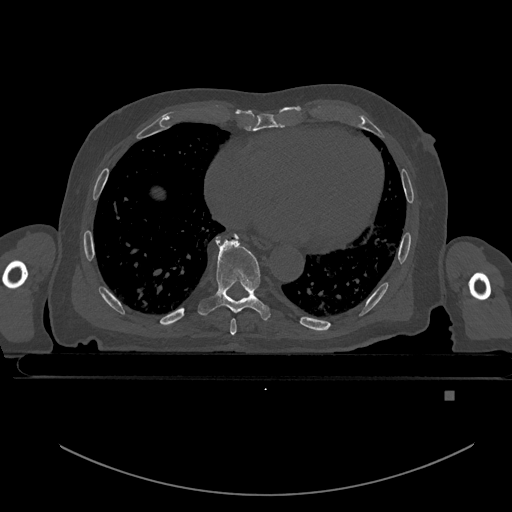
CT including the spine, one axial slice. Position 204 of 969 along the scan axis. Bone window (W 1800 / L 400 HU). 0.5 mm slice thickness. 512 × 512 image matrix. Male patient, age 82 years. From the clinical record (not read from this slice): primary cancer: prostate; vertebrae with lytic lesions (as recorded): T11, T9, T8, T2.
Annotated regions visible in this slice (semi-automatically segmented with operator editing):
- T7 vertebra: bounding box (x1, y1, x2, y2) in pixels: (230, 318, 236, 335)
- T8 vertebra: (198, 234, 272, 321)